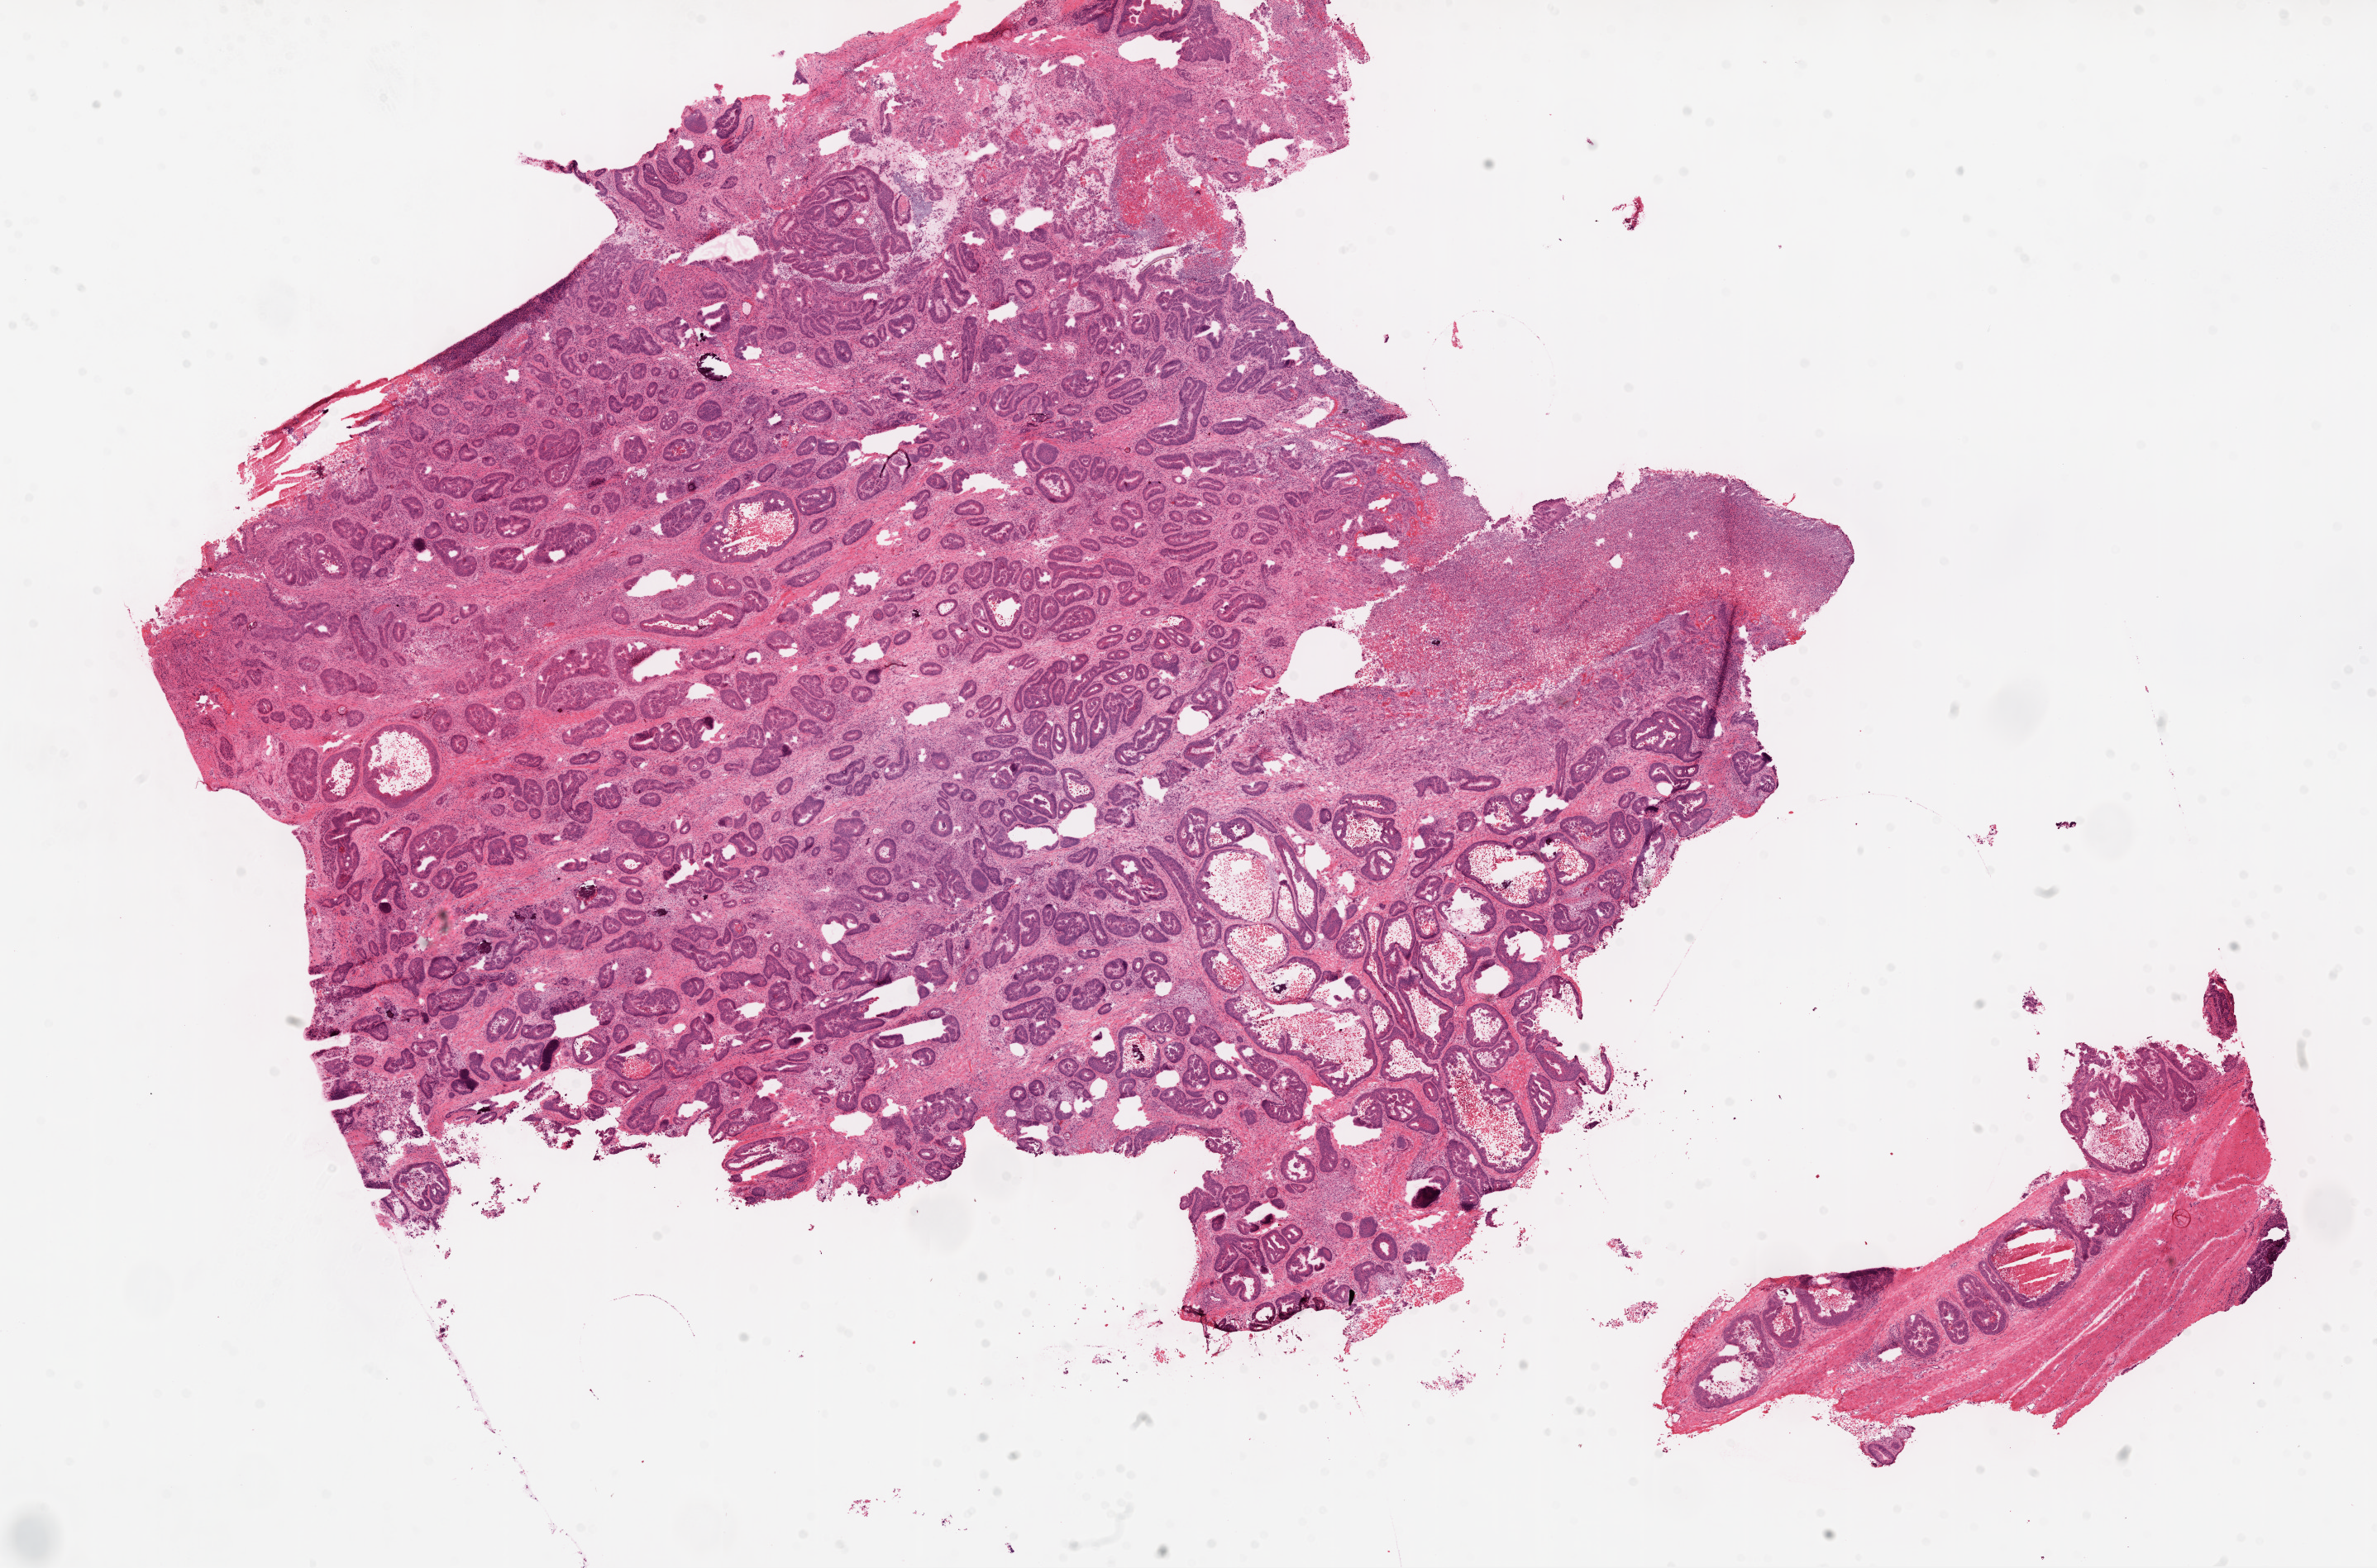
Whole-slide histology image, H&E, whole scanned area (about 23.1 x 15.2 mm) shown as a low-resolution overview, frozen section, colon, primary tumour sample. Female patient; age at initial diagnosis 82 years. Composition of this section per pathologist review: tumour cells 87%, tumour nuclei 75%, normal cells 0%, stromal cells 3%, necrosis 10%. Infiltration values recorded for this section: lymphocyte infiltration 5%, monocyte infiltration 1%, neutrophil infiltration 3%.
AJCC pathologic stage: IIIA. Pathologic diagnosis: Adenocarcinoma, NOS. Lymph nodes positive (case pathology): 1 of 18 examined.